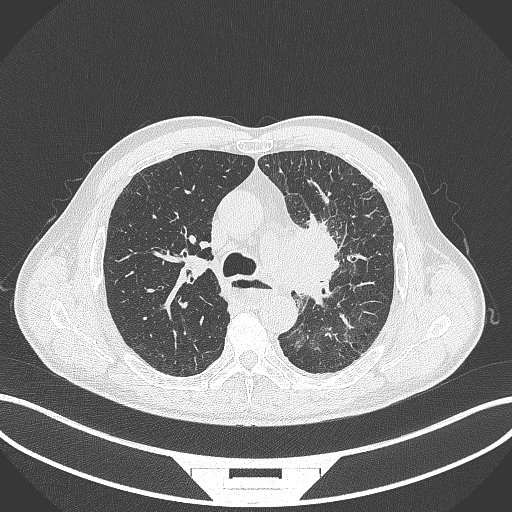
Chest CT, one axial slice. 120 kVp. Lung window (W 1500 / L -600 HU). 1 mm slice thickness. 512 × 512 image matrix, field of view 400 × 400 mm. Patient: male, 57 years. Case-level facts recorded for this patient, not image findings: clinical TNM (as recorded): T2a N1 M0.
Structures marked on this image (bounding box drawn by a radiologist):
- lung tumour (recorded histology: squamous cell carcinoma): bounding box (x1, y1, x2, y2) in pixels: (280, 214, 344, 303)